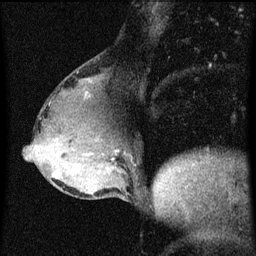
Breast MRI (dynamic contrast-enhanced), one sagittal slice; position 28 of 60 along the scan axis; dynamic contrast-enhanced series, image 2 of 3 at this slice position (ordered by acquisition); 1.5 T; TE 4.2 ms, TR 8 ms; 2 mm slice thickness; 256 × 256 image matrix, field of view 180 × 180 mm. Patient: female, 49 years.
Outlined on this slice (semi-automatic segmentation, software-assisted and operator-edited):
- analysis volume of interest (the breast-tissue region the enhancement analysis was run in; not a lesion): bounding box (x1, y1, x2, y2) in pixels: (51, 158, 96, 185)
- tumour enhancement mask (voxels above the 70 % enhancement threshold inside the analysis volume of interest): (54, 166, 81, 177)